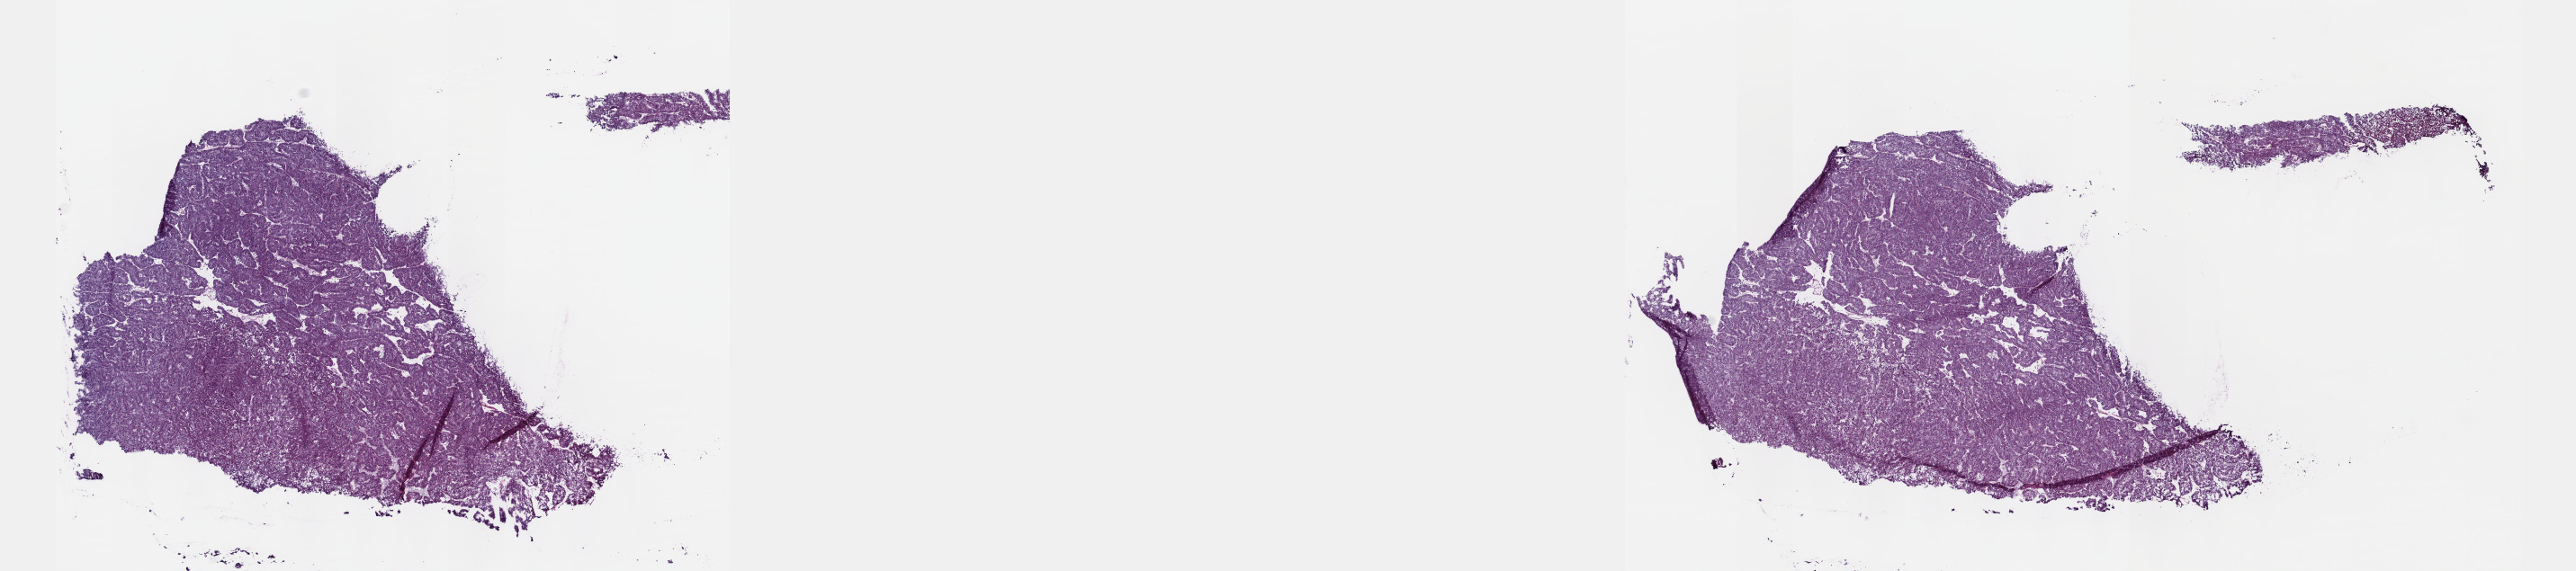
Whole-slide histology image, Hematoxylin and eosin (H&E) stained, a low-resolution overview of the entire scanned area, about 23.1 x 5.1 mm (slide scanned at 40x). Frozen section from the top of the tissue portion. Sample: primary tumour, kidney. Patient sex: female. Composition of this section per pathologist review: tumour cells 100%, tumour nuclei 95%, normal cells 0%, stromal cells 0%, necrosis 0%. Inflammatory infiltration, as recorded: lymphocyte infiltration 0%, monocyte infiltration 0%, neutrophil infiltration 0%.
• histologic diagnosis: Papillary adenocarcinoma, NOS
• AJCC pathologic stage: I